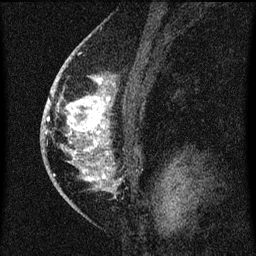
Breast MRI (dynamic contrast-enhanced), one sagittal slice; slice 41 of 60 in the series (ordered by position); dynamic contrast-enhanced series, image 2 of 3 at this slice position (ordered by acquisition); 1.5 T; TE 4.2 ms, TR 8 ms; 2 mm slice thickness; 256 × 256 image matrix, field of view 180 × 180 mm. Patient: female, 46 years.
Structures marked on this image (semi-automatic segmentation, software-assisted and operator-edited):
- analysis volume of interest (the breast-tissue region the enhancement analysis was run in; not a lesion): box from (x=53, y=68) to (x=116, y=195) px
- tumour enhancement mask (voxels above the 70 % enhancement threshold inside the analysis volume of interest): (x=54, y=70)–(x=115, y=187)